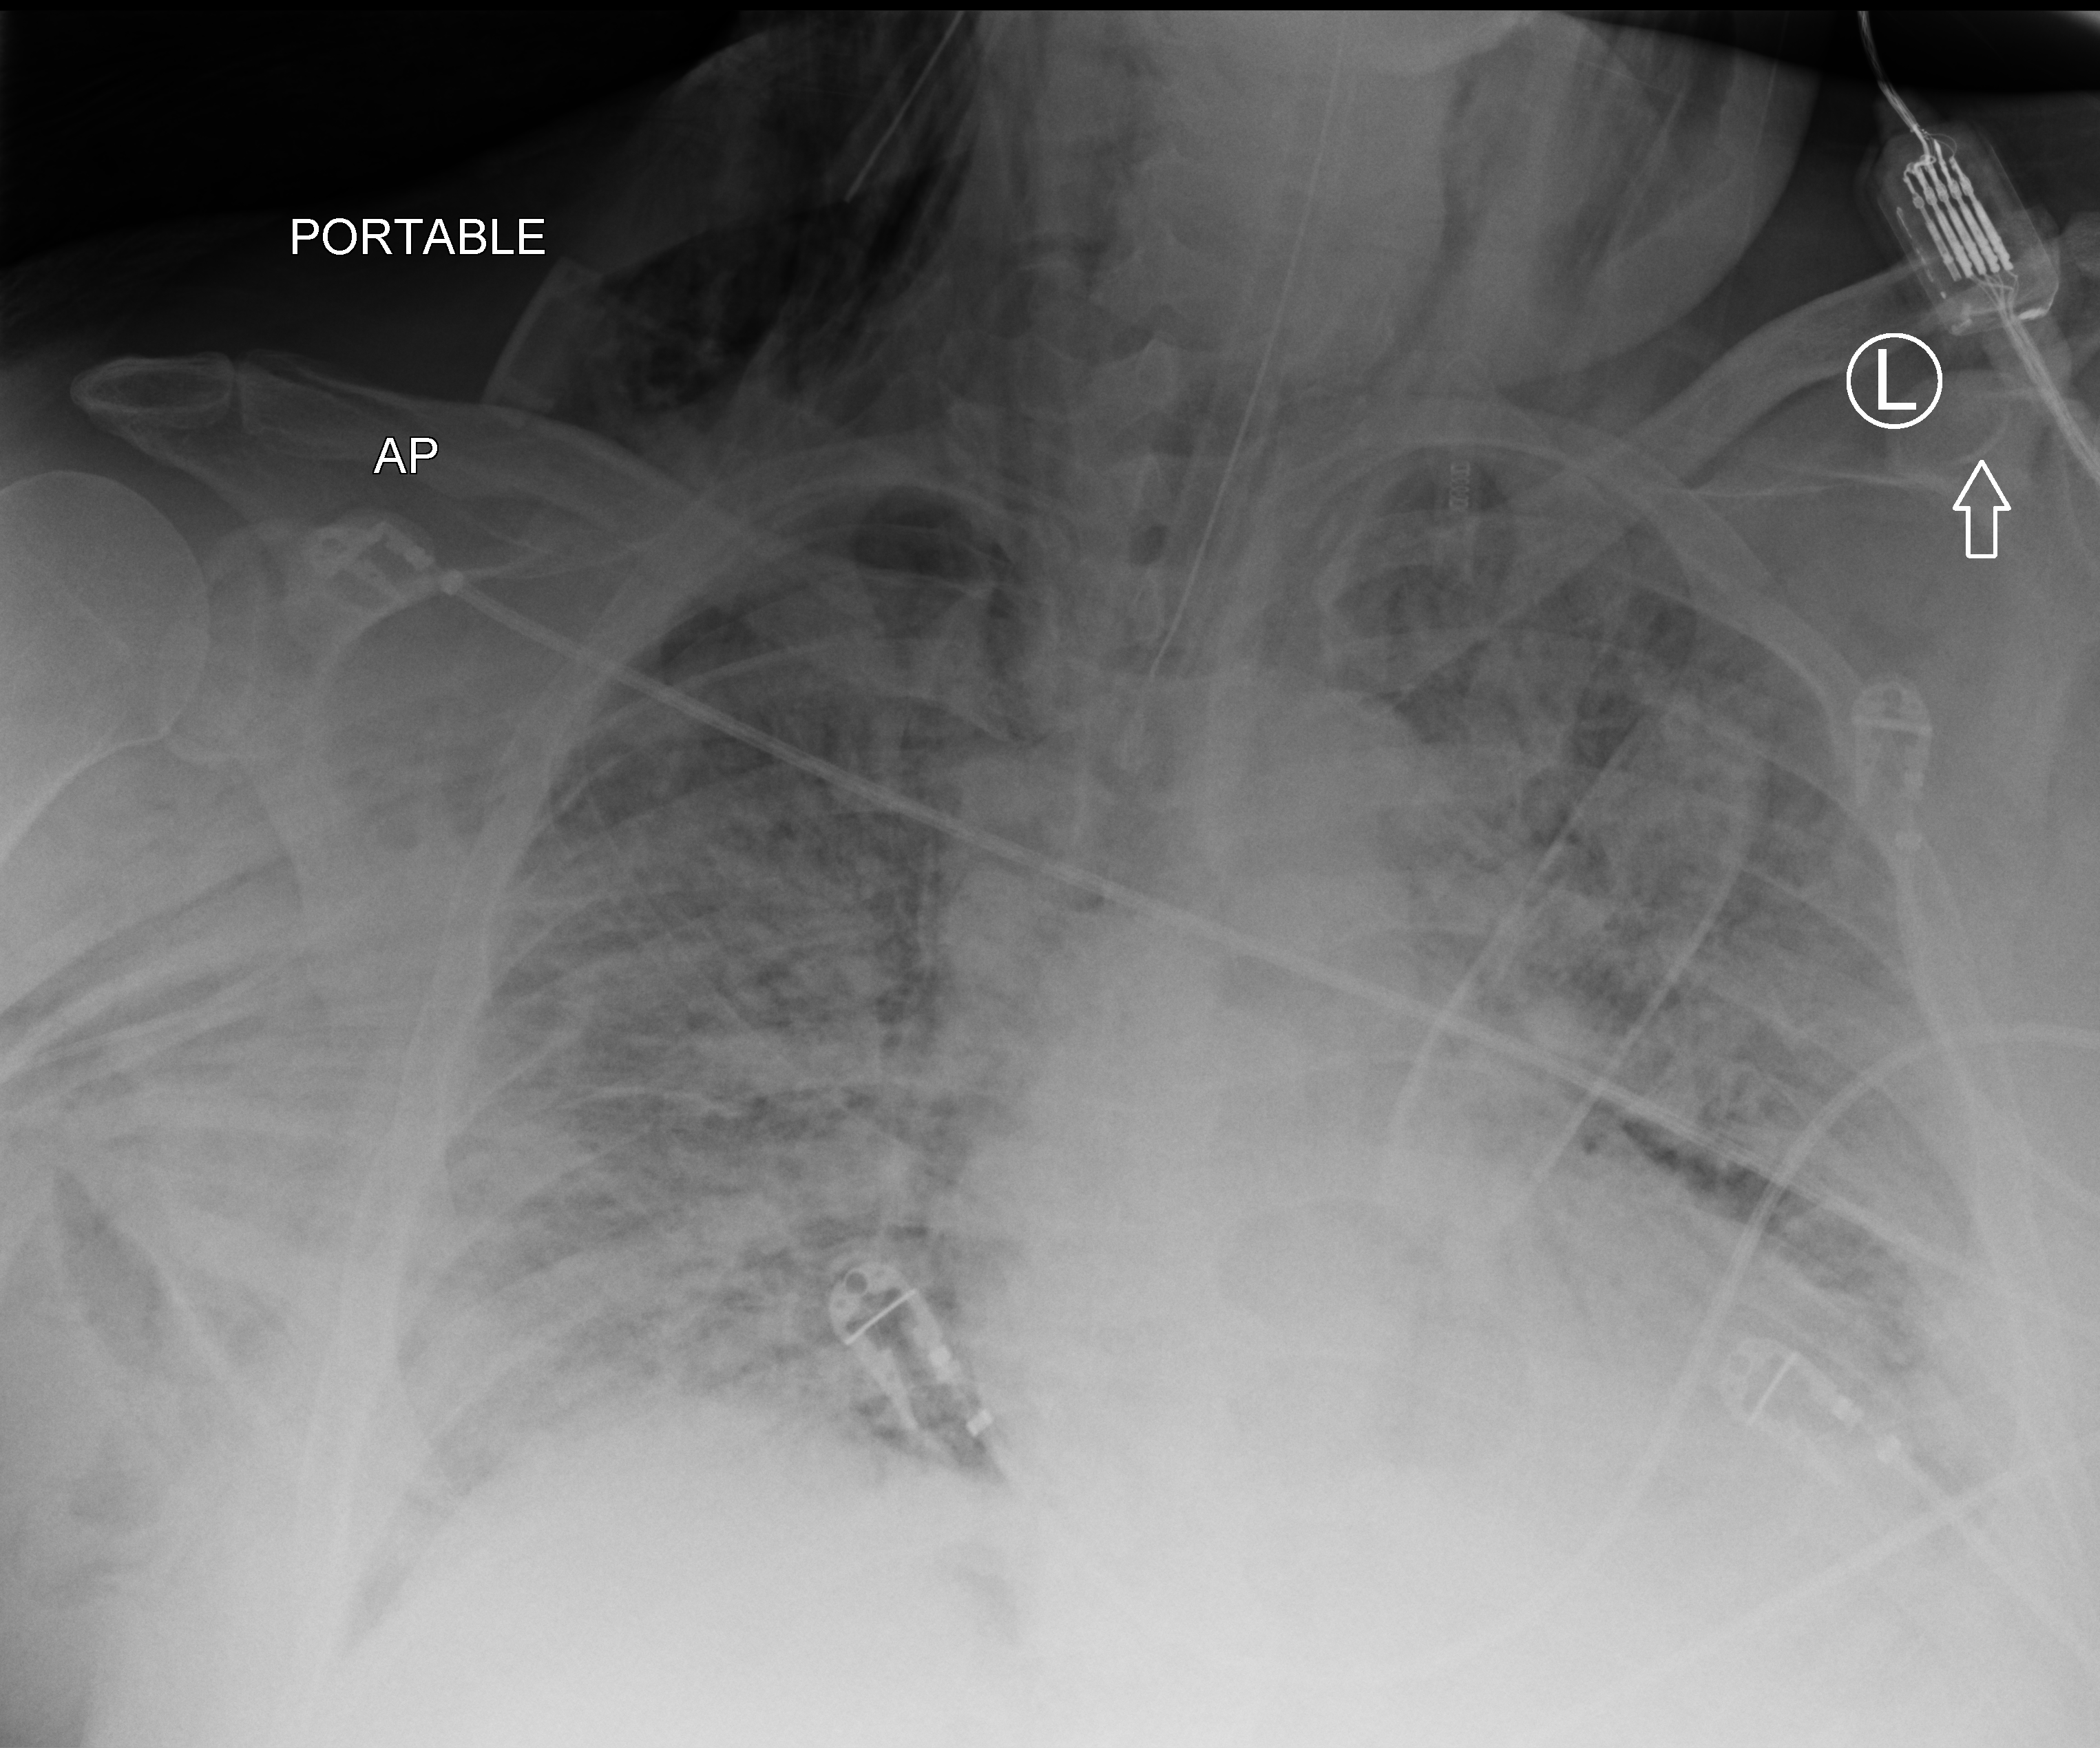
Bedside chest radiograph (computed radiography), anteroposterior (AP) projection. Adult patient hospitalised with COVID-19, age 18–59 years.
From the hospital-stay record, not from the radiograph (when in the stay this image was taken is not recorded): diabetes (admission record): yes; mechanically ventilated during this hospital stay: yes.